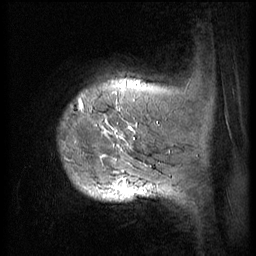
Breast MRI (dynamic contrast-enhanced), one sagittal slice; slice 9 of 56 in the series (ordered by position); 3 images stored at this slice position (order not interpretable as contrast timing); 1.5 T; TE 4.2 ms, TR 9 ms; 2.5 mm slice thickness; 256 × 256 image matrix, field of view 180 × 180 mm. Female patient, age 49 years. Case-level facts recorded for this patient, not image findings: setting: breast cancer imaged before/during neoadjuvant chemotherapy; receptor status: HER2-positive.
Structures marked on this image (semi-automatic segmentation, software-assisted and operator-edited):
- analysis volume of interest (the breast-tissue region the enhancement analysis was run in; not a lesion): bounding box <51,79,152,203> (left, top, right, bottom; pixels)
- tumour enhancement mask (voxels above the 140 % enhancement threshold inside the analysis volume of interest): <79,84,147,198>